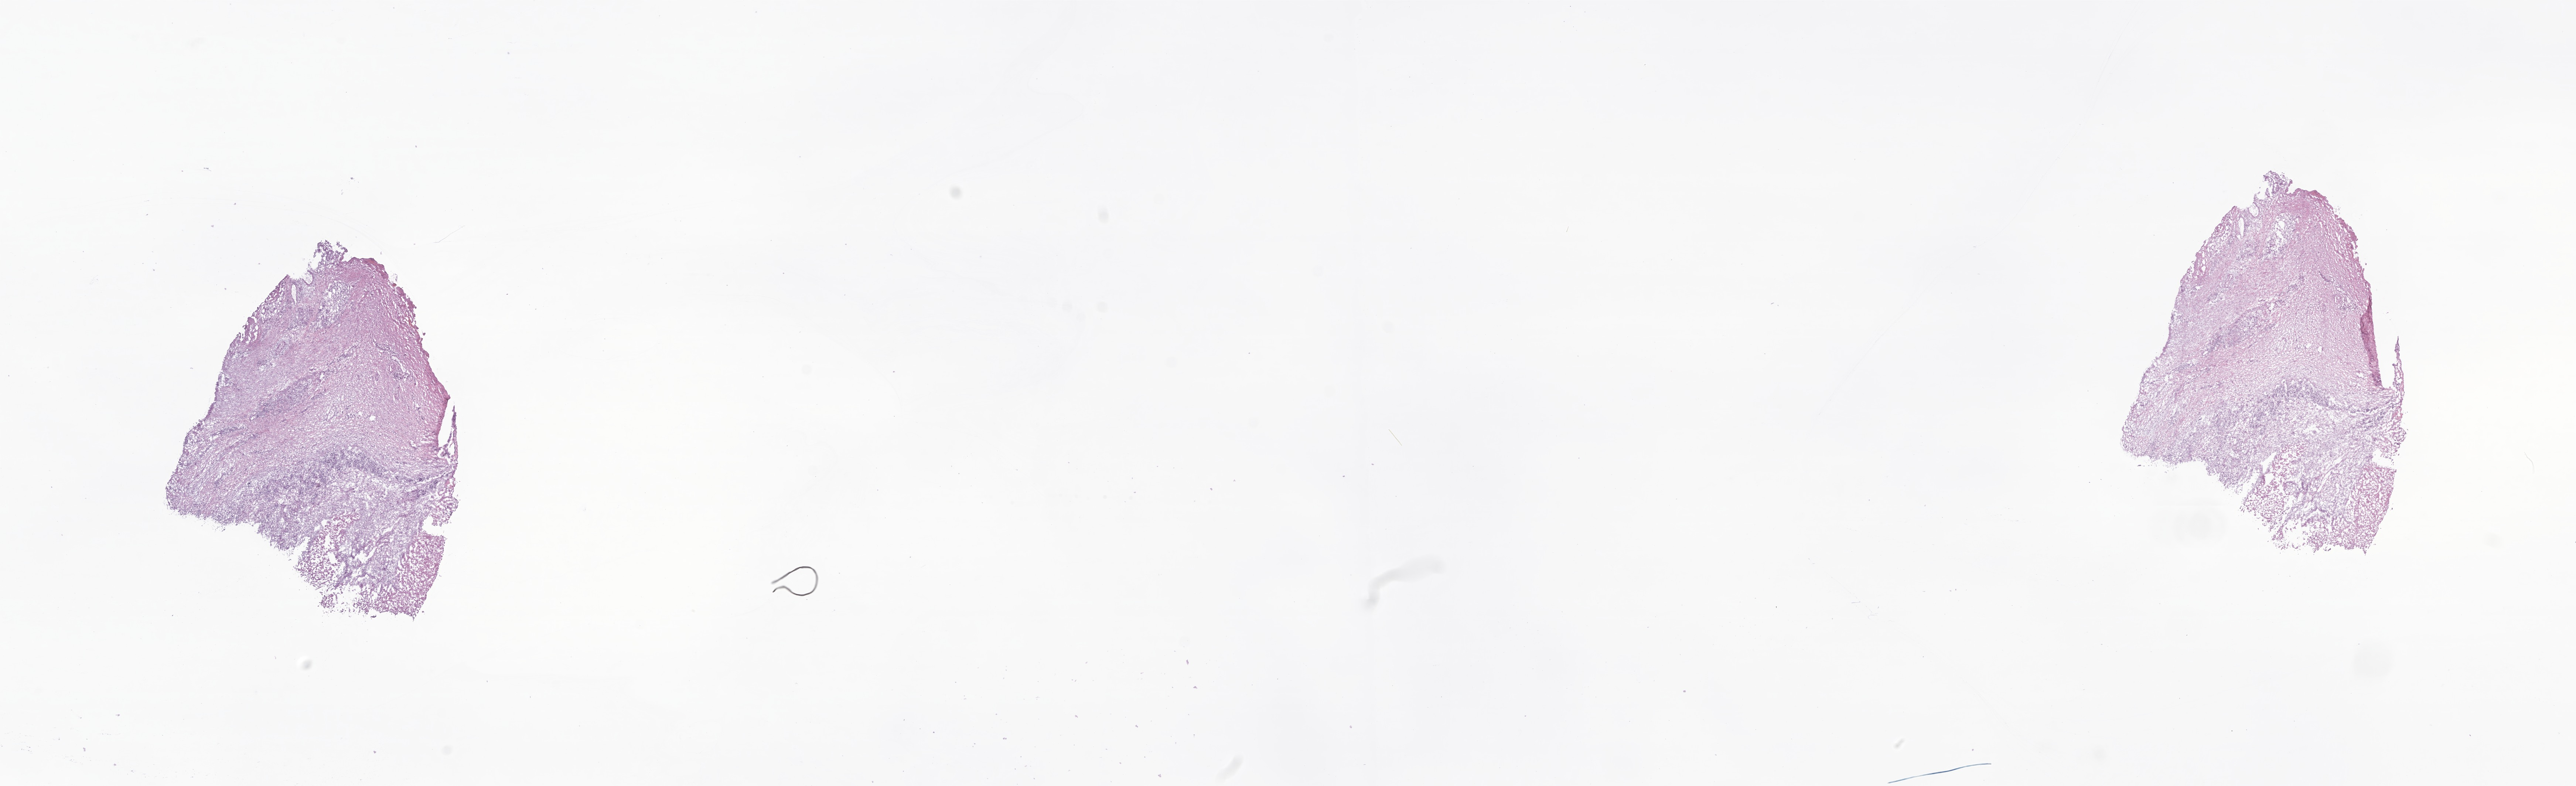
Haematoxylin and eosin whole-slide image of tumor tissue from the nerve of thorax — a low-resolution overview of the entire scanned area, about 29.4 x 9.0 mm, cryosection (OCT / tissue freezing medium). Patient male; age 68 months (5 years 8 months).
- tissue or organ of origin (case record): peripheral nerves and autonomic nervous system of thorax
- diagnosis (ICD-O-3 morphology term): Neuroblastoma, NOS